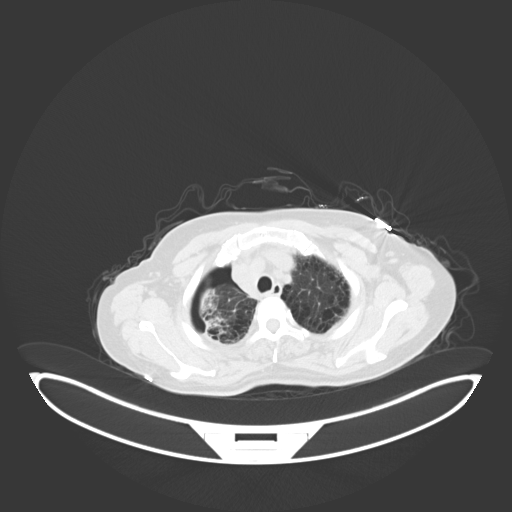
Chest CT, one axial slice; reconstruction kernel B30f; 120 kVp; lung window (W 1500 / L -600 HU); 512 × 512 image matrix, field of view 500 × 500 mm. Female patient, age 64 years. Case-level facts recorded for this patient, not image findings: clinical TNM (as recorded): T3 N3 M0.
Structures marked on this image (bounding box drawn by a radiologist):
- lung tumour (recorded histology: squamous cell carcinoma): box from (x=194, y=282) to (x=233, y=340) px